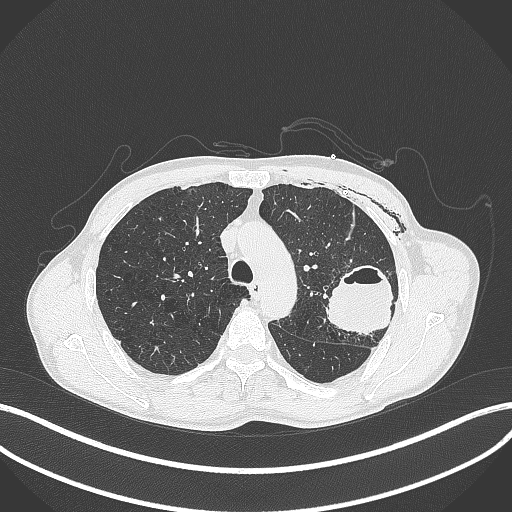
Chest CT, one axial slice. Position 294 of 457 along the scan axis. 120 kVp. Lung window (W 1500 / L -600 HU). 1 mm slice thickness. 512 × 512 image matrix, field of view 400 × 400 mm. Male patient, age 58 years. From the clinical record (not read from this slice): clinical TNM (as recorded): T3 N0 M0.
Structures marked on this image (rectangle marked by the reading radiologist):
- lung tumour (recorded histology: adenocarcinoma): bounding box [x1, y1, x2, y2] px = [324, 261, 396, 337]